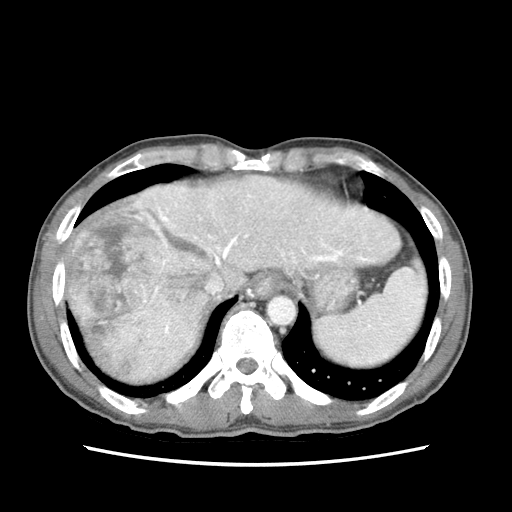
Contrast-enhanced abdominal CT (liver protocol), one axial slice; position 61 of 79 along the scan axis; 120 kVp; soft-tissue window (W 400 / L 40 HU); 2.5 mm slice thickness; 512 × 512 image matrix, field of view 320 × 320 mm. Case-level facts recorded for this patient, not image findings: diagnosis: hepatocellular carcinoma (patient treated with transarterial chemoembolisation; whether this scan precedes or follows treatment is not stated here); TNM stage (as recorded): Stage-IIIB; Child-Pugh class: A.
Annotated regions visible in this slice (semi-automatic segmentation, software-assisted and operator-edited):
- abdominal aorta: bounding box [x1, y1, x2, y2] px = [268, 297, 295, 324]
- liver parenchyma outside the tumour (the mass and vessels are separate outlines, so this box may not span the whole liver): [66, 174, 400, 384]
- mass: [64, 192, 214, 382]
- liver vessels: [144, 185, 380, 340]